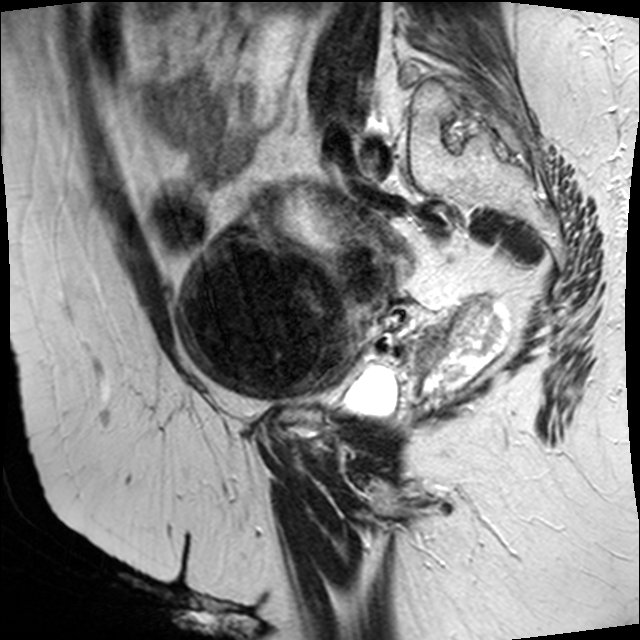
Pelvic MRI for cervical cancer, one sagittal slice. T2-weighted. 1.5 T. TE 89 ms, TR 4610 ms. 640 × 640 image matrix, field of view 260 × 260 mm. Patient: female, 50 years.
Outlined on this slice (outlined manually by an expert reader):
- uterus and cervix: box from (x=178, y=193) to (x=509, y=391) px